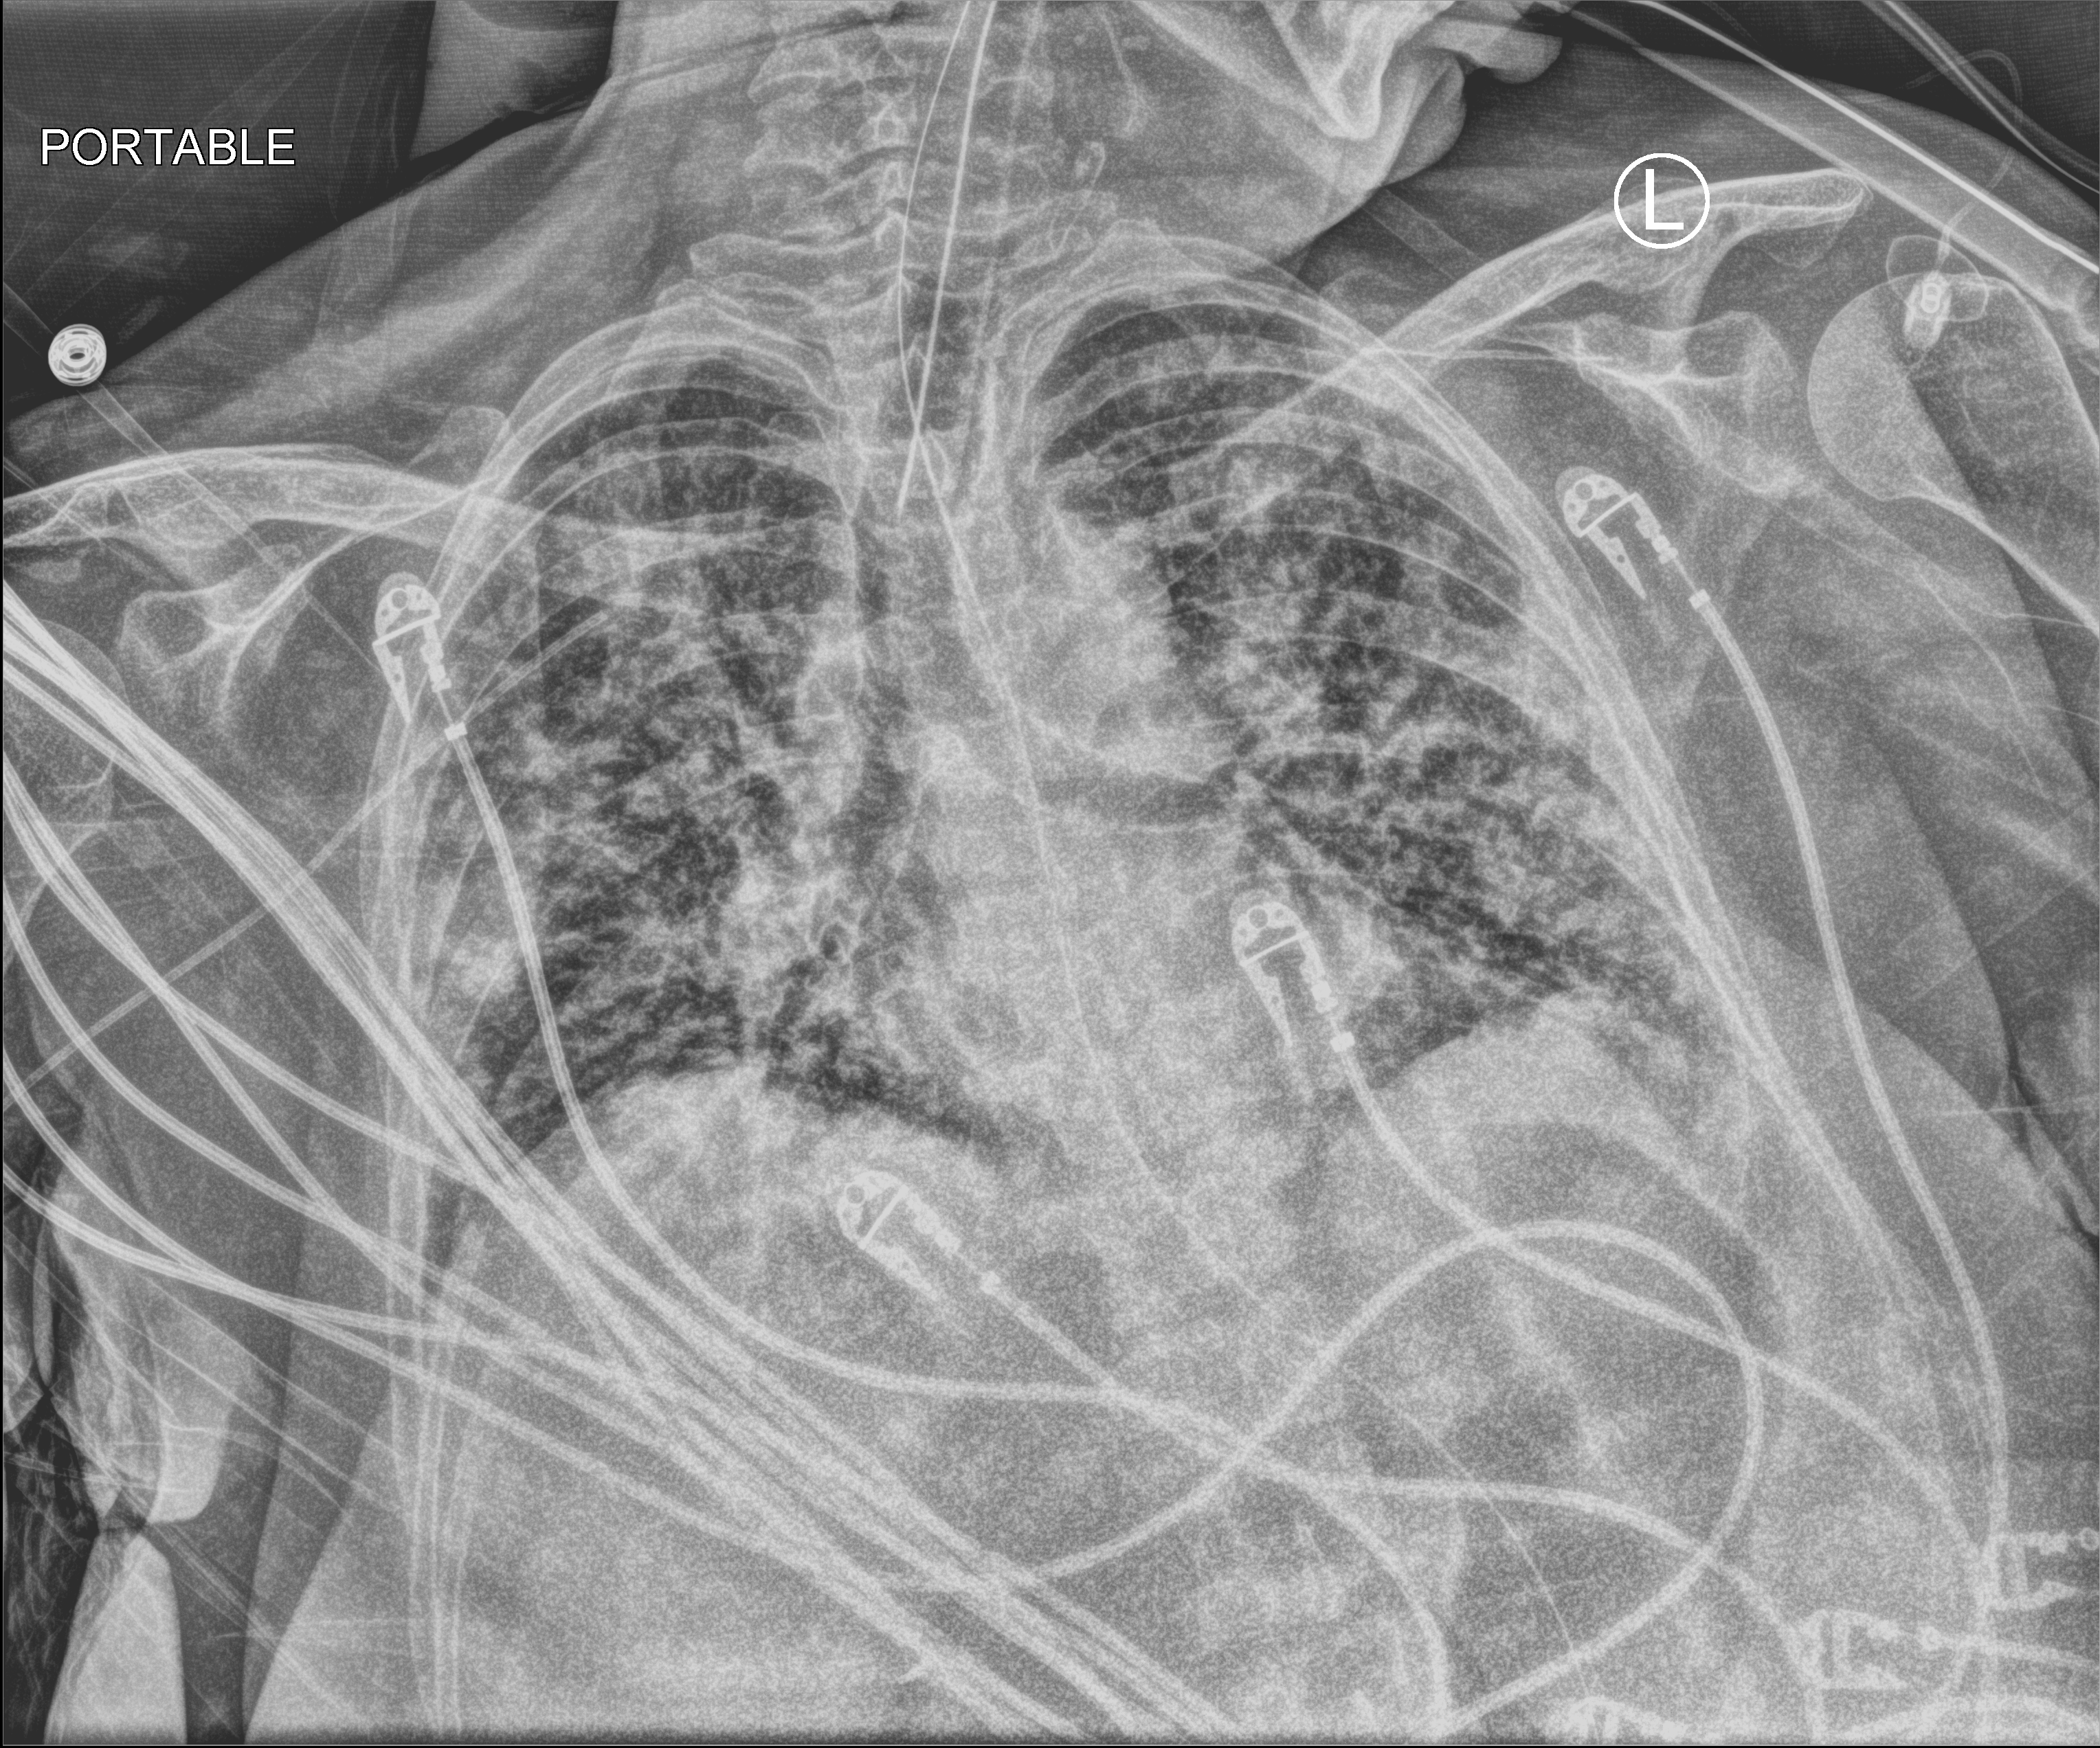
Bedside chest radiograph (computed radiography), anteroposterior (AP) projection. Patient hospitalised with COVID-19; female, aged 18–59 years.
Admission-level facts for this patient (not findings on this image; timing relative to this image not recorded):
- length of hospital stay: 22 days
- mechanically ventilated during this hospital stay: yes
- admitted to intensive care during this hospital stay: yes